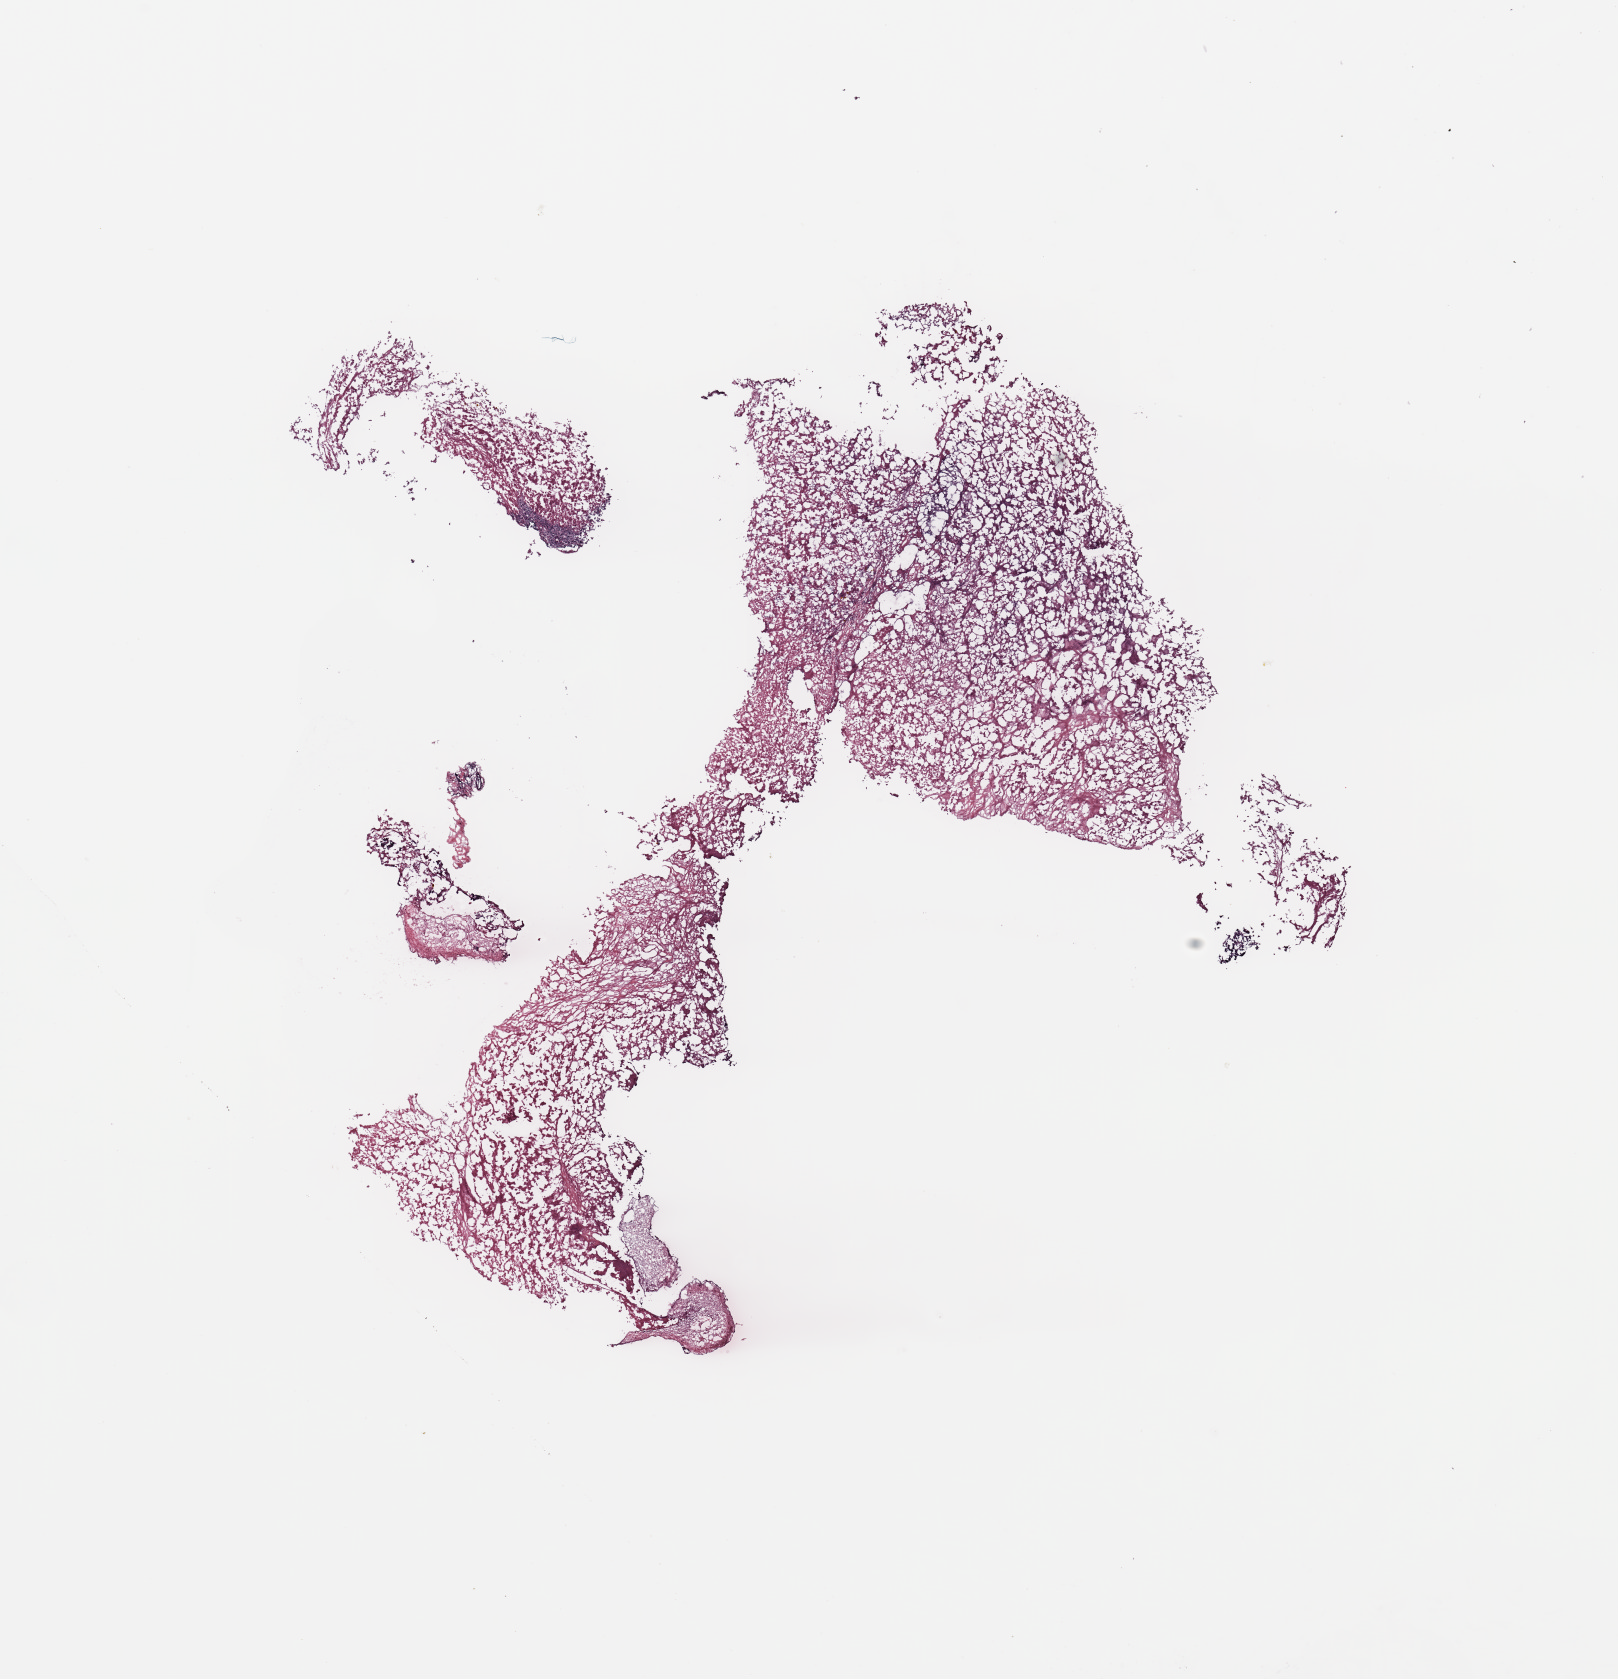
Whole-slide histology image, Hematoxylin and eosin (H&E) stained, shown as a low-resolution overview of the whole scanned area (about 12.8 x 13.3 mm); breast, tumour tissue. Patient: female, age 58 years.
Histologic diagnosis: Infiltrating duct carcinoma, NOS. AJCC pathologic stage: II.